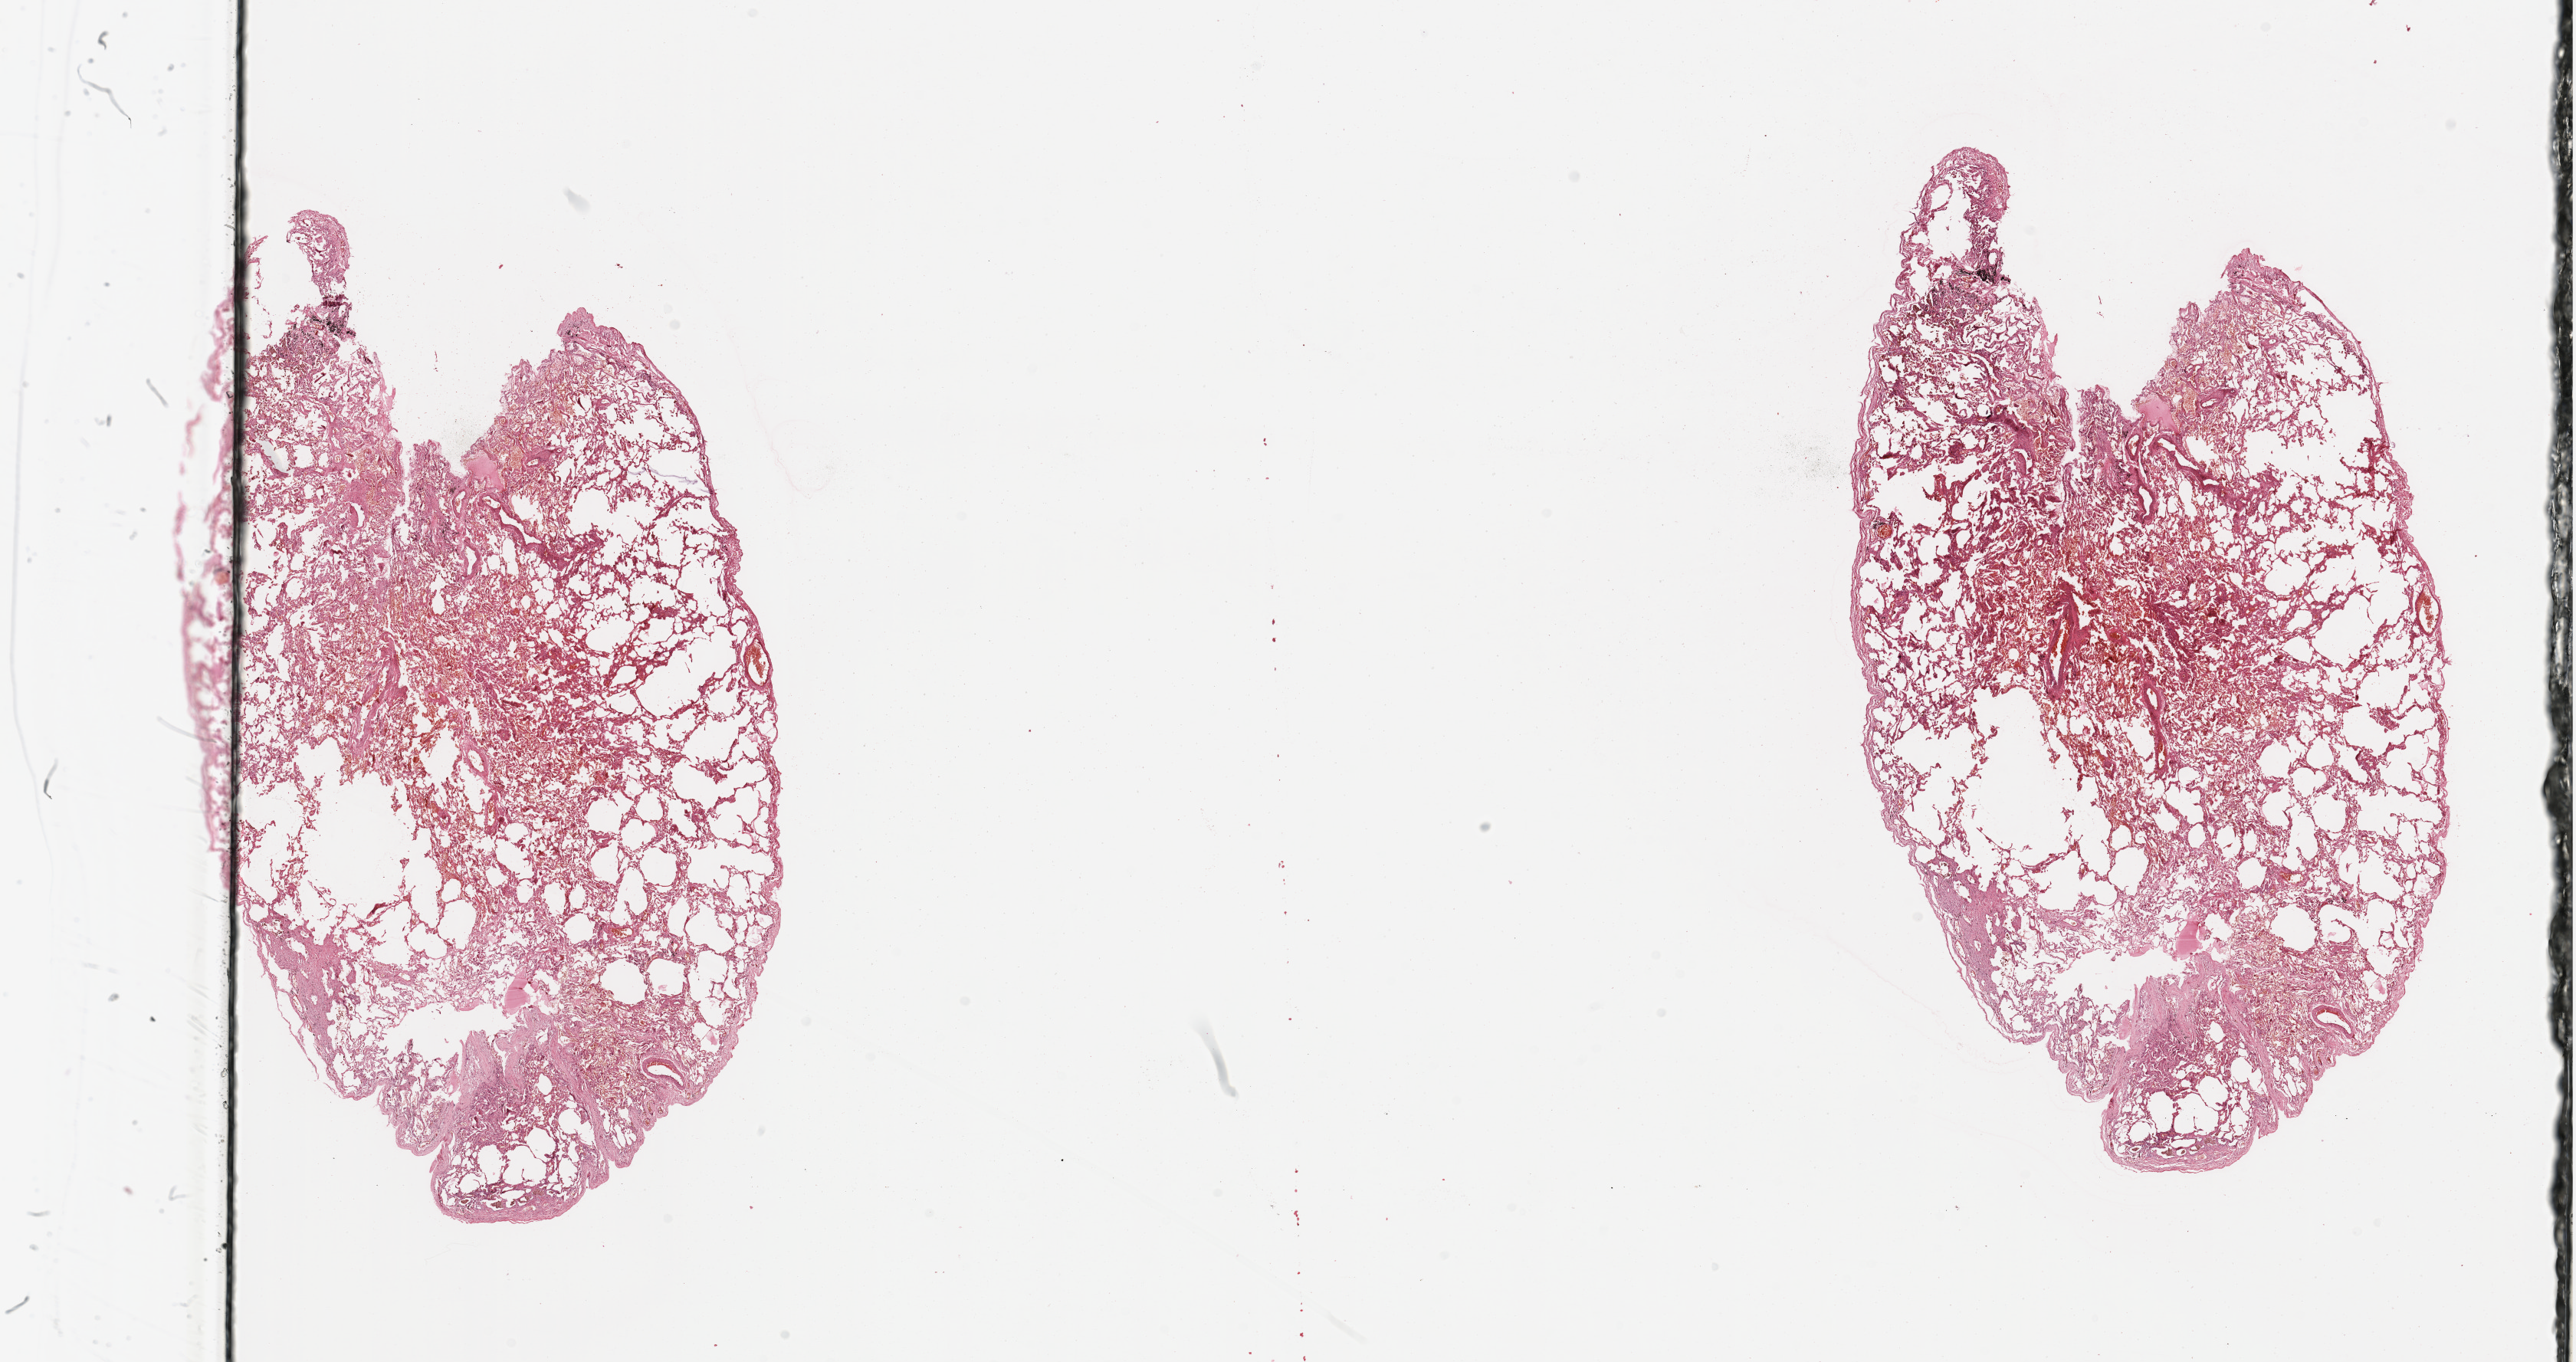
Whole-slide histology image, H&E-stained — a low-resolution overview of the entire scanned area, about 26.6 x 14.1 mm (from a 20x scan), normal (non-tumour) tissue sample, sampled site: lung. Male, 54 y/o.
This section: normal (non-tumour) tissue from the same patient. Patient diagnosis: Adenocarcinoma, NOS.